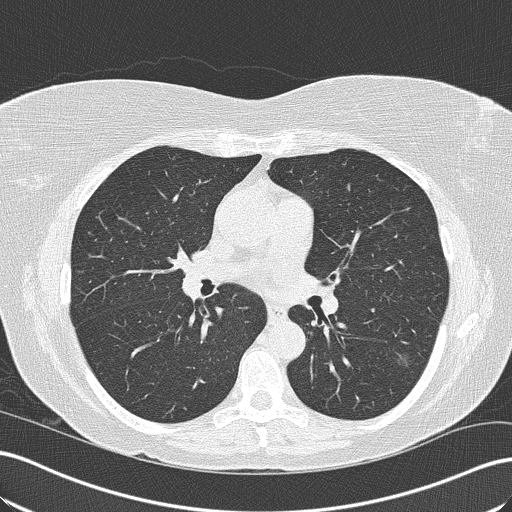
Axial slice from a low-dose chest CT screening exam. Second annual screen. Lung window (W 1500 / L -600 HU). Slice 82 of 165 in the series. 512 × 512 image matrix, field of view 358 × 358 mm. Female, age 57 years at enrolment.
Lesion marked by an expert reader, bounding box (x1, y1, x2, y2) in pixels: (381, 336, 429, 382). The screening reader recorded 6 non-calcified nodules or masses ≥4 mm on this exam (left lower lobe, right upper lobe, right upper lobe, right upper lobe, right lower lobe, right upper lobe); which of them this box marks is not recorded. Participant outcome: lung cancer diagnosed 482 days after this screen — bronchiolo-alveolar adenocarcinoma, NOS, left lower lobe, well differentiated (G1), stage IA (AJCC 6th edition), 16 mm at pathology.